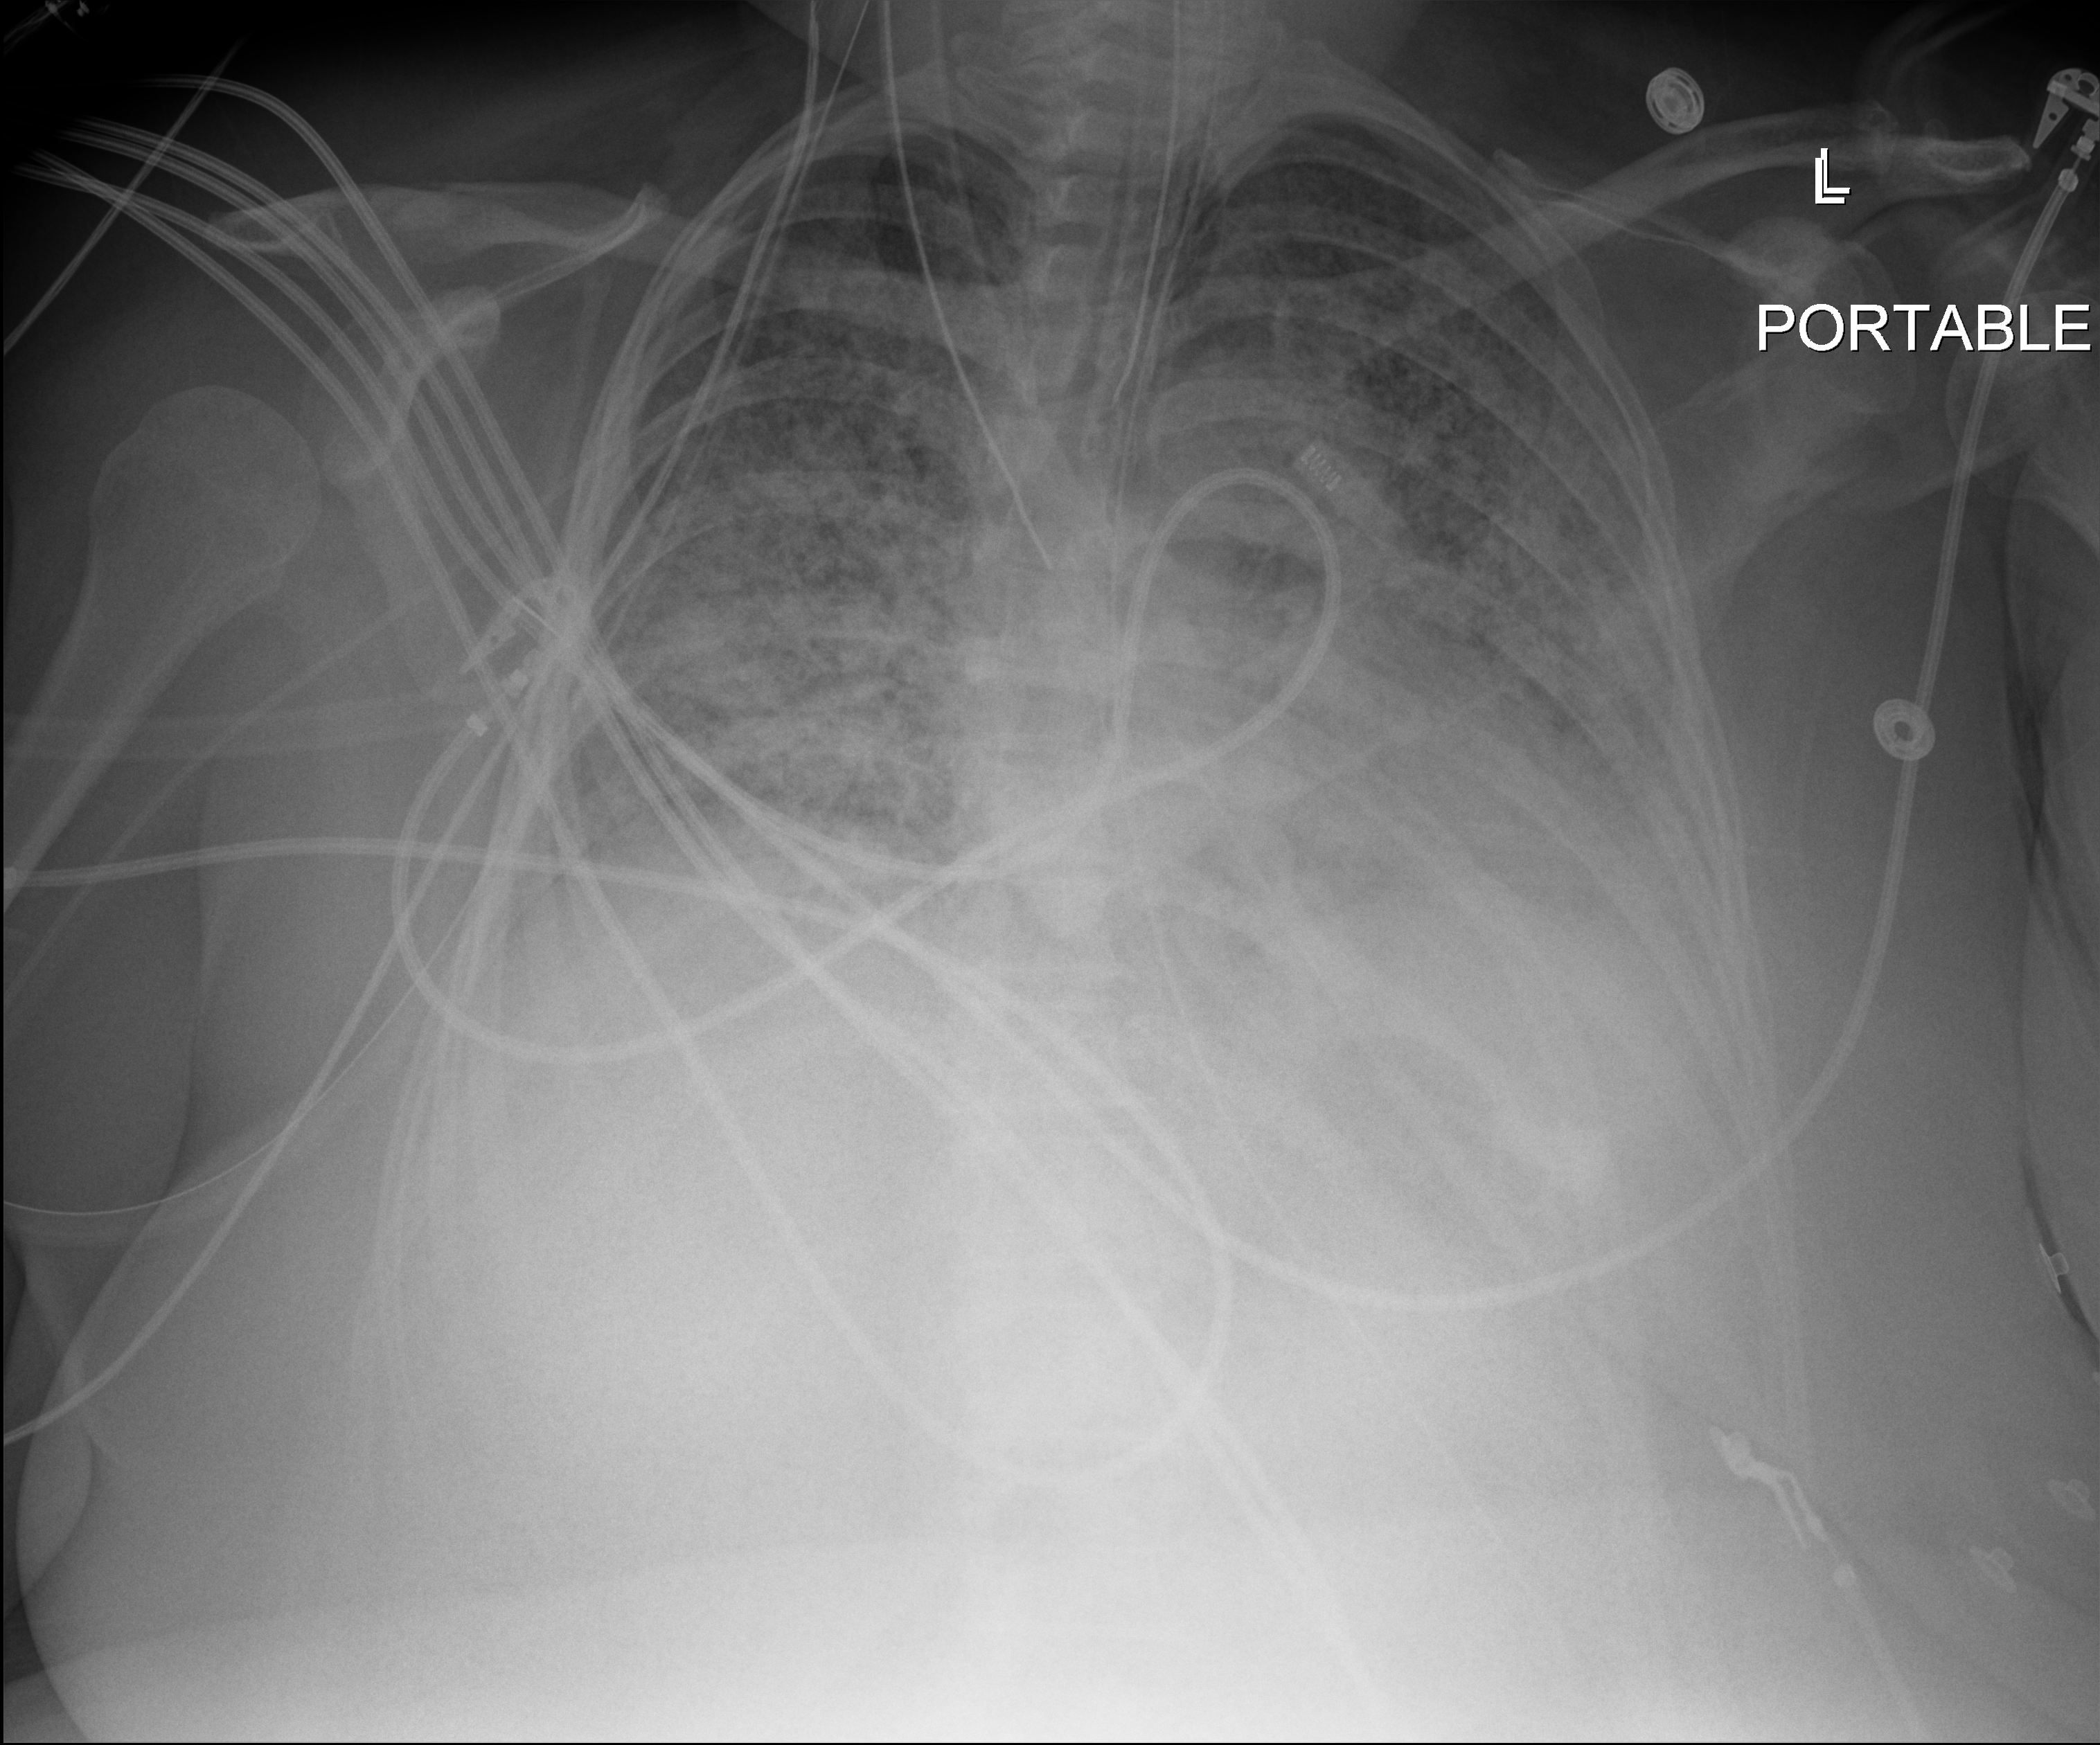
Bedside chest radiograph (digital radiography). Patient hospitalised with COVID-19; female, aged 18–59 years.
From the hospital-stay record, not from the radiograph (when in the stay this image was taken is not recorded): smoking status (admission record): never; length of hospital stay: 95 days.